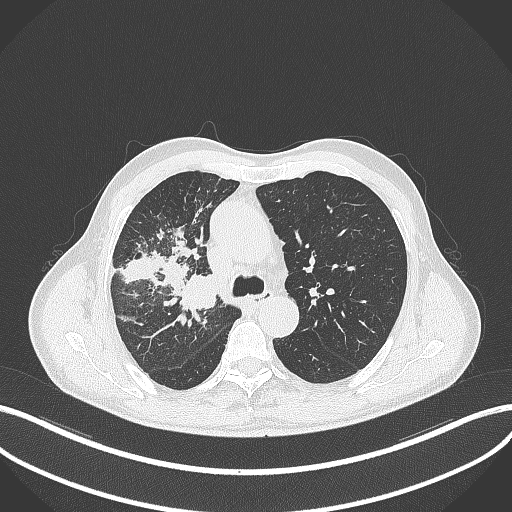
Chest CT, one axial slice; position 330 of 490 along the scan axis; lung window (W 1500 / L -600 HU); 512 × 512 image matrix, field of view 400 × 400 mm. Male patient, age 69 years. Case-level facts recorded for this patient, not image findings: clinical TNM (as recorded): T2a N0 M0.
Annotated regions visible in this slice (rectangle marked by the reading radiologist):
- lung tumour (recorded histology: adenocarcinoma): bounding box <181,272,223,313> (left, top, right, bottom; pixels)